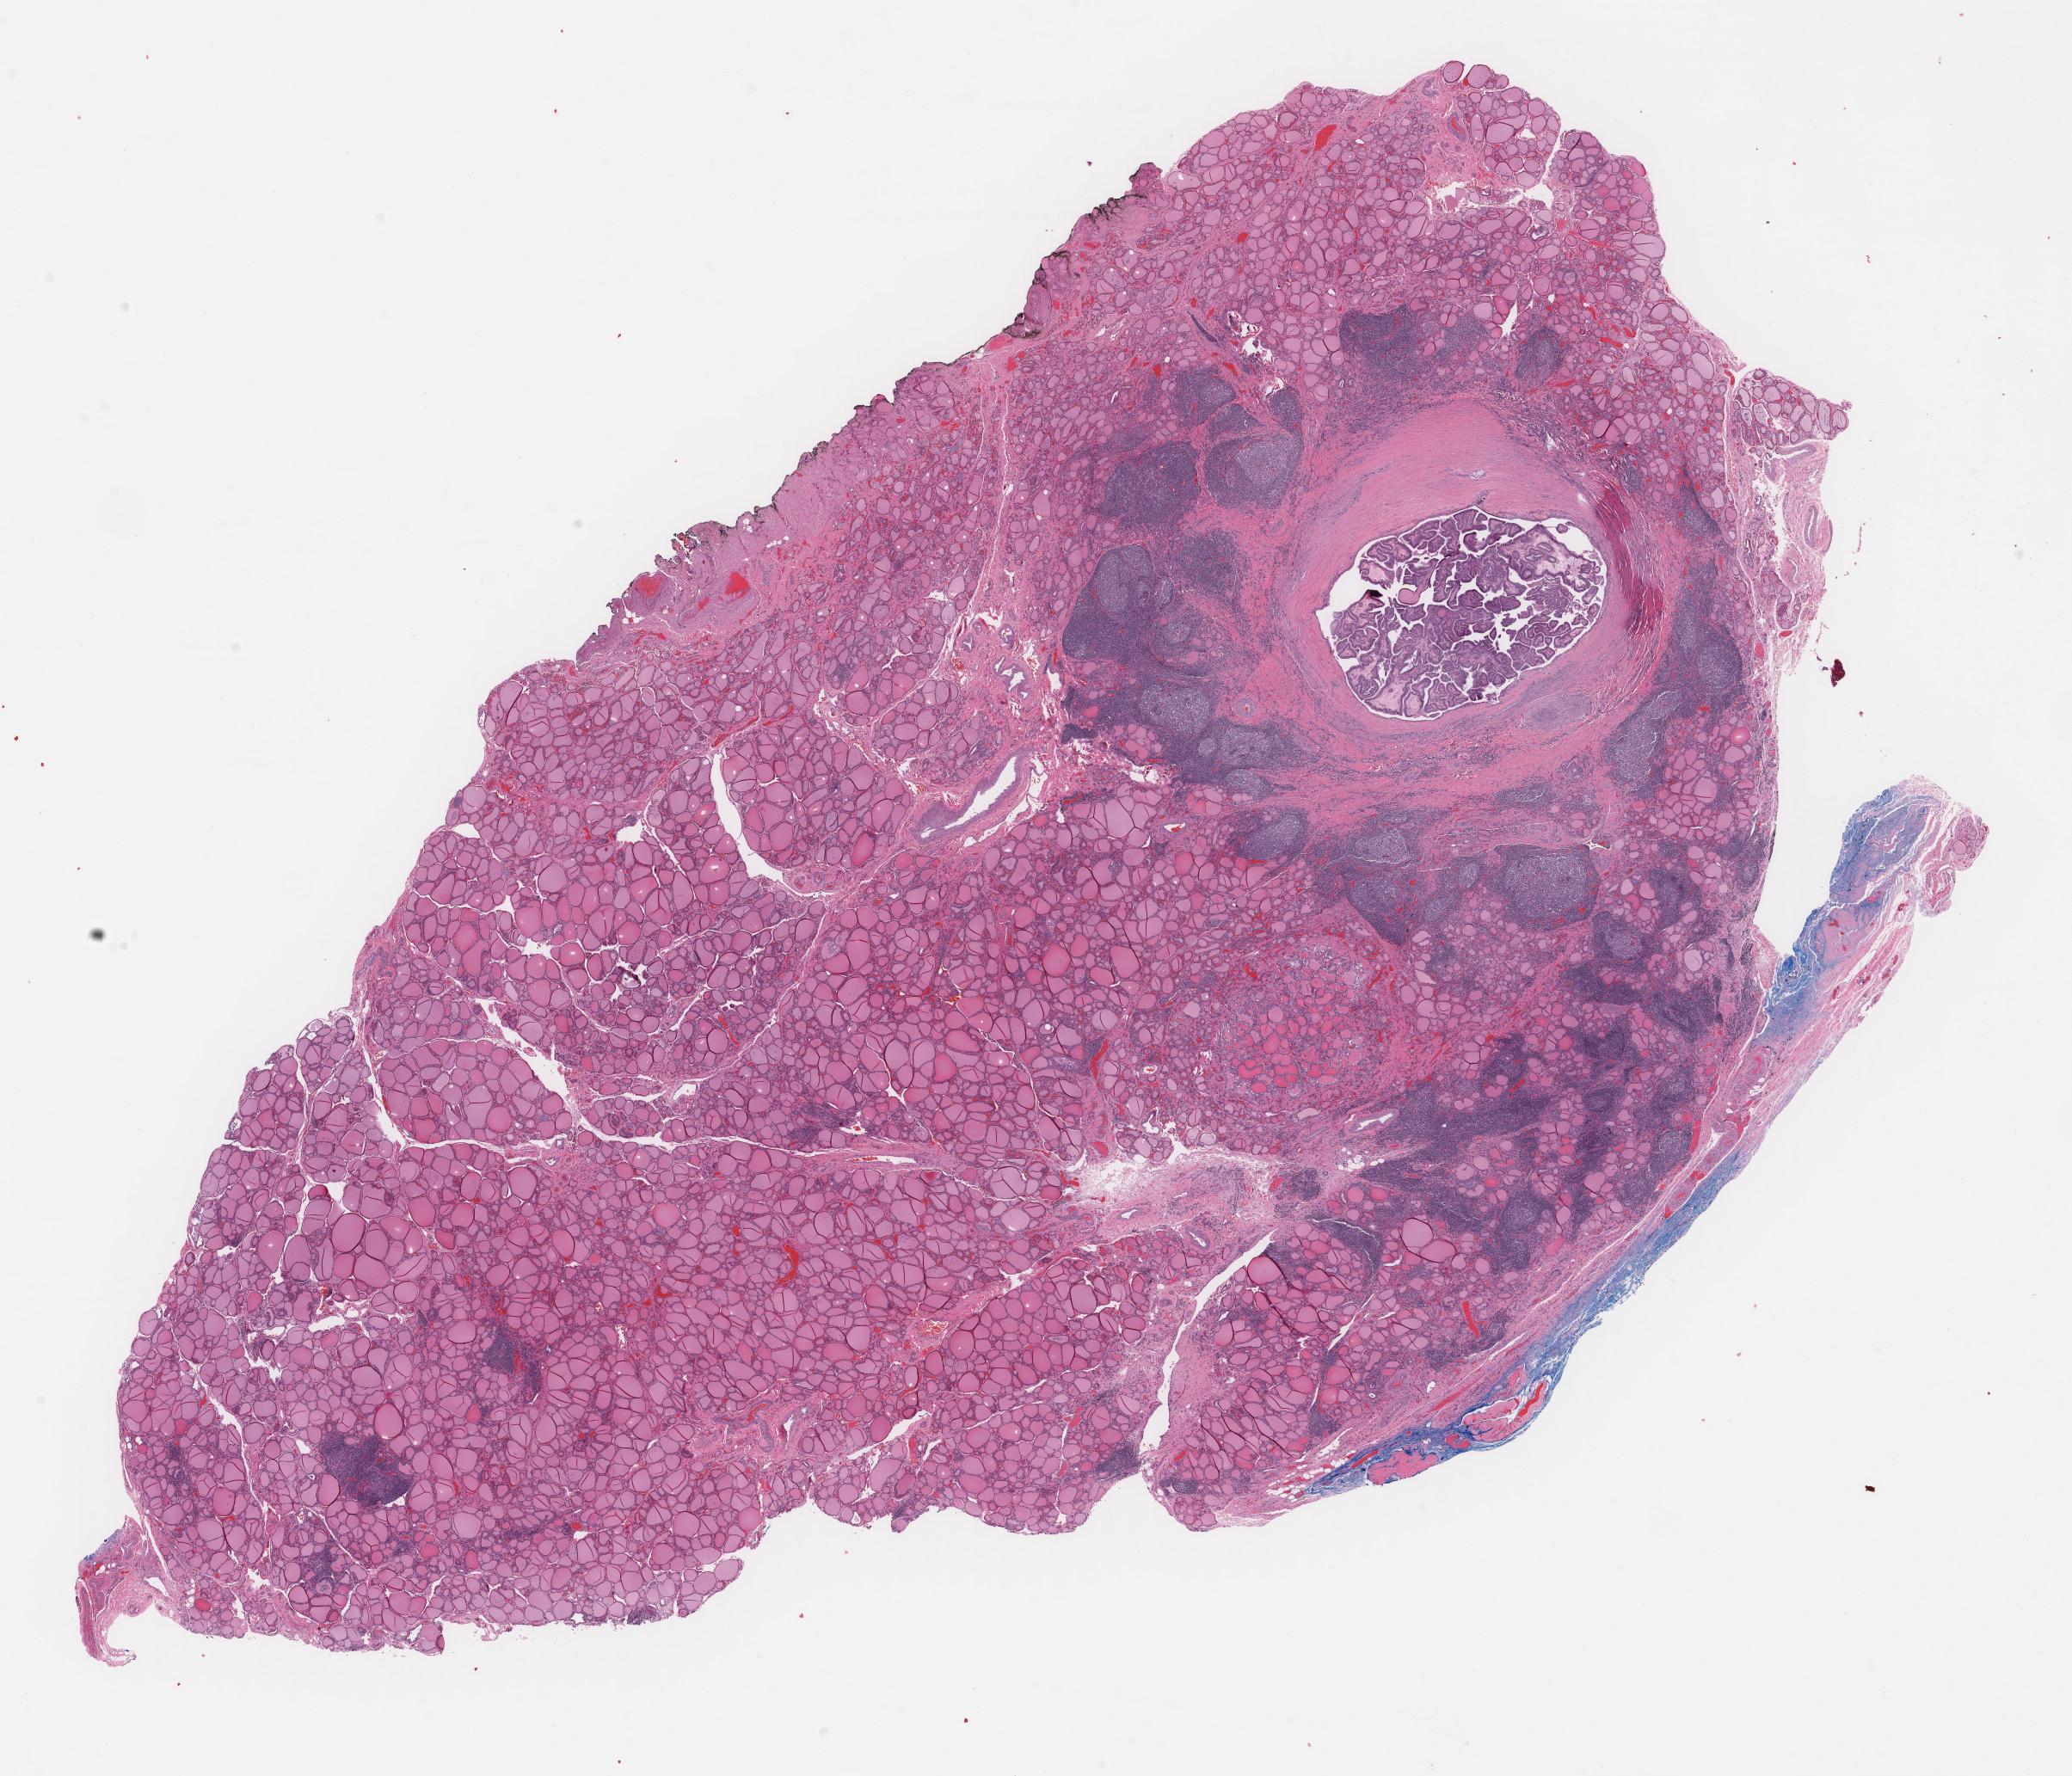
Whole-slide histology image, H&E, shown as a low-resolution overview of the whole scanned area (about 19.1 x 16.4 mm). FFPE section. Thyroid, primary tumour sample. Female, age 65 years at initial diagnosis.
- laterality: right
- AJCC pathologic stage: III
- lymph nodes positive (case pathology): 1 of 5 examined
- diagnosis: Papillary carcinoma, columnar cell
- TNM: T1b N1a M0